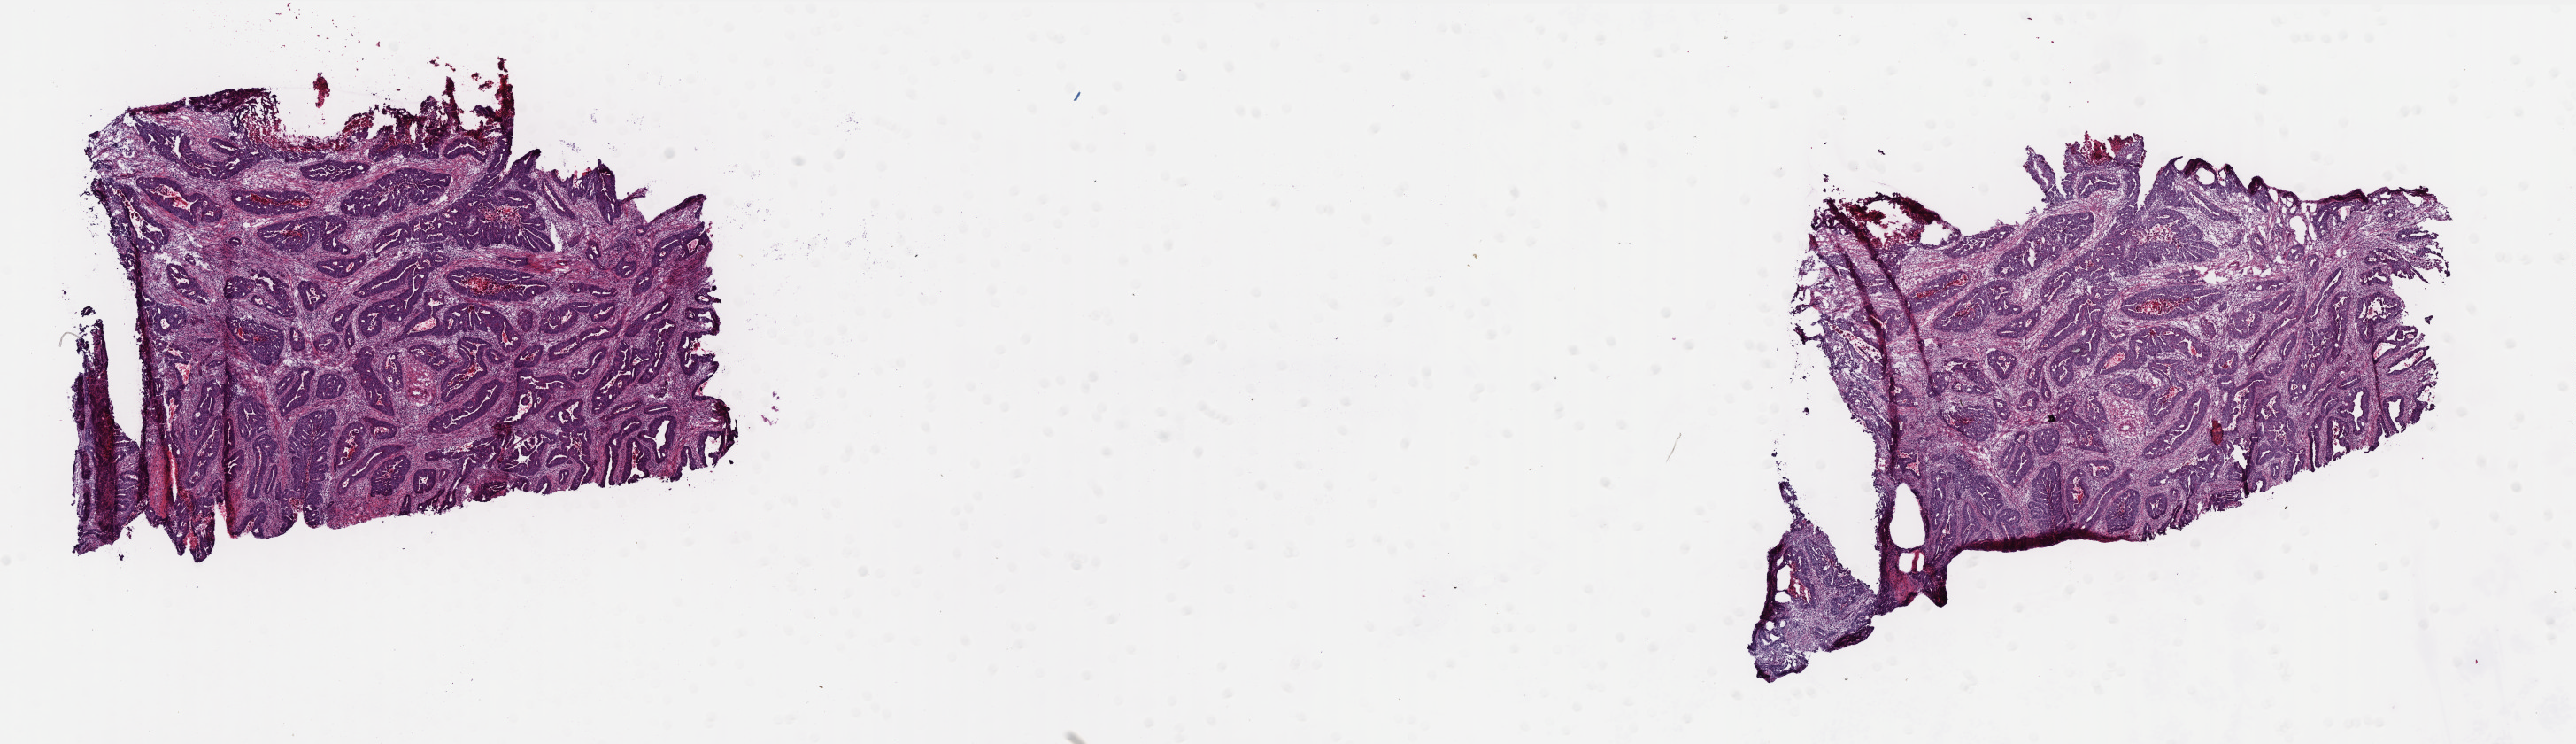
H&E-stained whole-slide image — shown as a low-resolution overview of the whole scanned area (about 23.3 x 6.7 mm, slide scanned at 40x), frozen section, colon, primary tumour sample. Female patient; age at initial diagnosis 82 years. Pathologist review of this section (percent, as recorded): tumour cells 97%, tumour nuclei 80%, normal cells 0%, stromal cells 0%, necrosis 3%. Infiltration values recorded for this section: lymphocyte infiltration 2%, monocyte infiltration 1%, neutrophil infiltration 2%.
* TNM: T3 N1 M1
* lymph nodes positive (case pathology): 4 of 16 examined
* AJCC pathologic stage: IV
* histologic diagnosis: Adenocarcinoma, NOS (cecum)